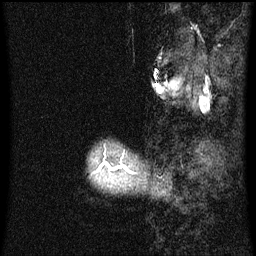
Breast MRI (dynamic contrast-enhanced), one sagittal slice; position 8 of 60 along the scan axis; dynamic contrast-enhanced series, image 2 of 3 at this slice position (ordered by acquisition); 1.5 T; TE 4.2 ms, TR 8 ms; 2 mm slice thickness; 256 × 256 image matrix. Patient: female, 50 years.
Structures marked on this image (semi-automatically segmented with operator editing):
- analysis volume of interest (the breast-tissue region the enhancement analysis was run in; not a lesion): bounding box [x1, y1, x2, y2] px = [94, 149, 138, 187]
- tumour enhancement mask (voxels above the 70 % enhancement threshold inside the analysis volume of interest): [117, 166, 131, 173]